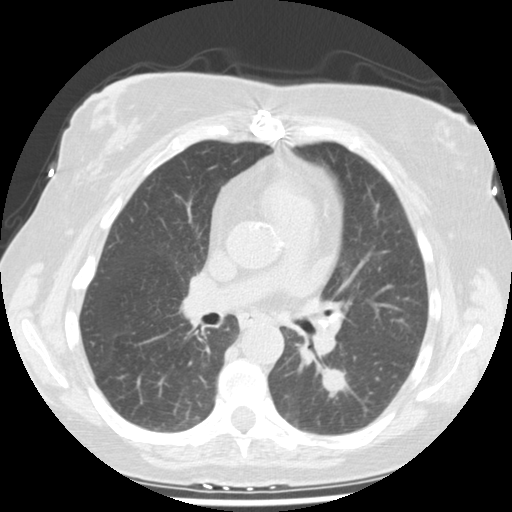
Low-dose screening chest CT, one axial slice; reconstruction kernel STANDARD; lung window (W 1500 / L -600 HU); 512 × 512 image matrix, field of view 326 × 326 mm.
Annotated regions visible in this slice (expert manual segmentation):
- lesion 1 (tumor, lower lobe of left lung): bounding box [x1, y1, x2, y2] px = [319, 366, 349, 394]